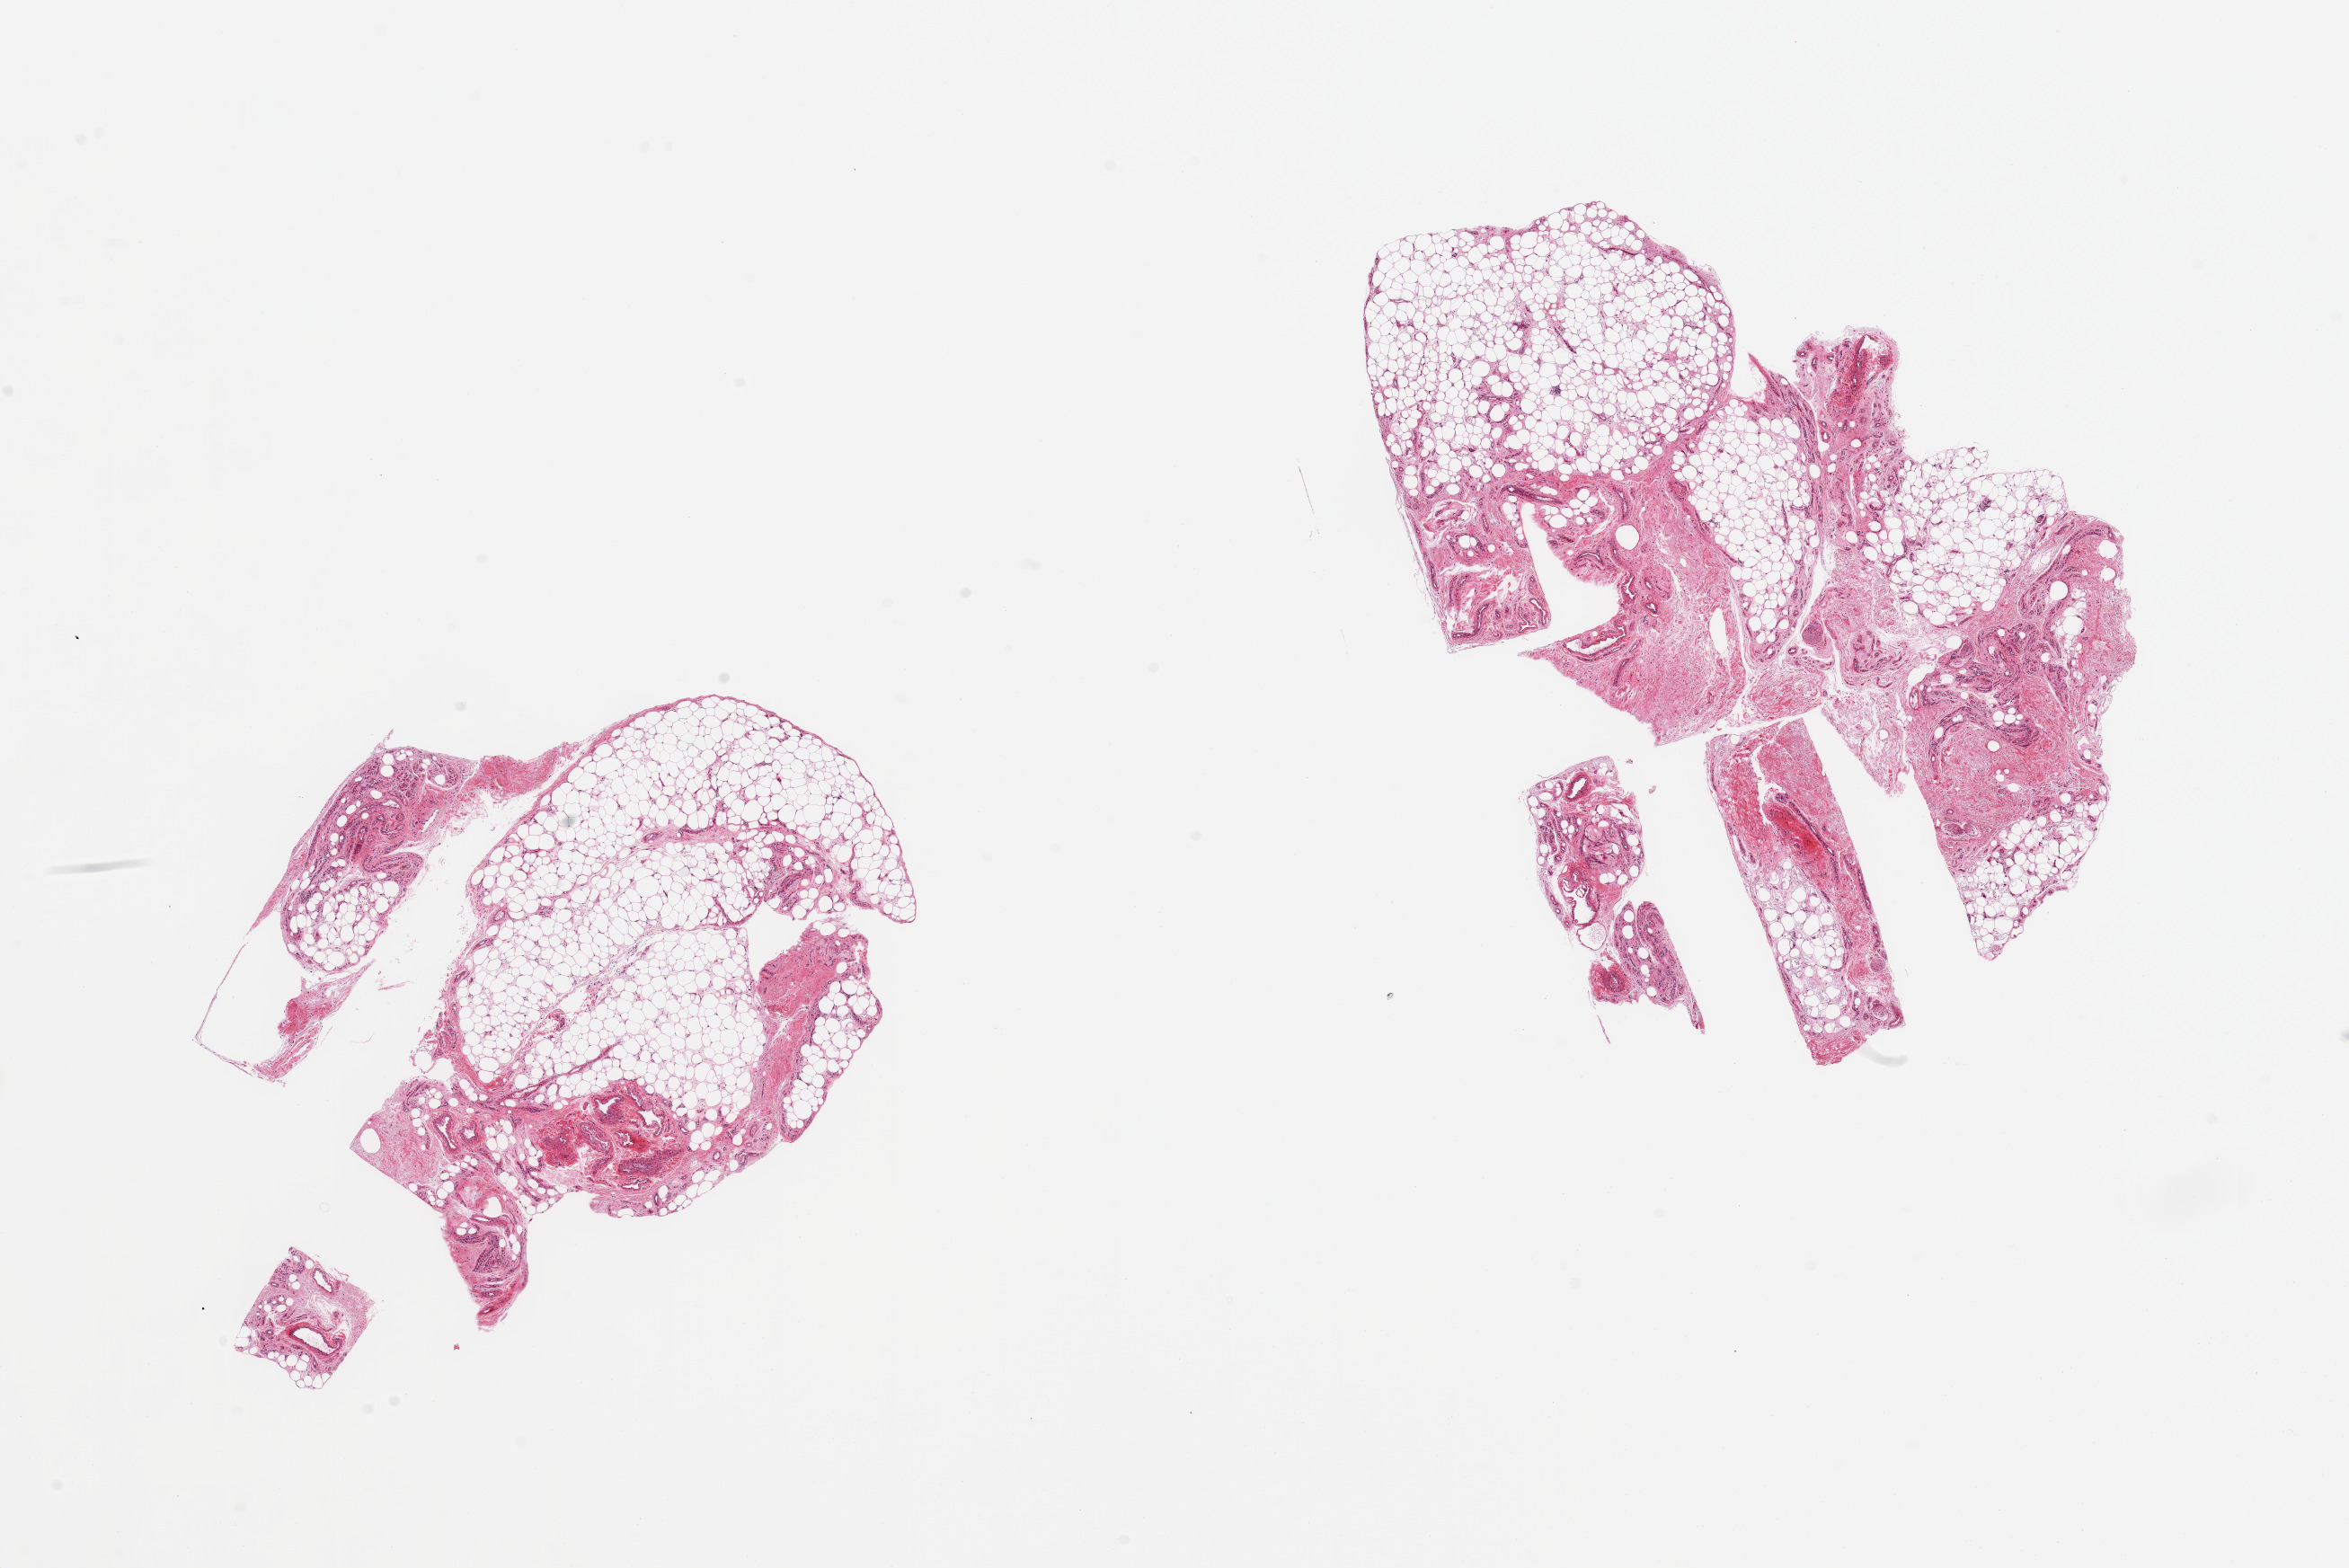
Digitized haematoxylin and eosin-stained section — shown as a low-resolution overview of the whole scanned area (about 20.7 x 13.8 mm, acquisition: 20x scan). PAXgene-fixed, paraffin-embedded tissue. Section of adipose tissue (target tissue). Donor tissue sample. Donor sex: female.
• pathologist's review note for this sample: 2 pieces; 20-40% fibrovascular component